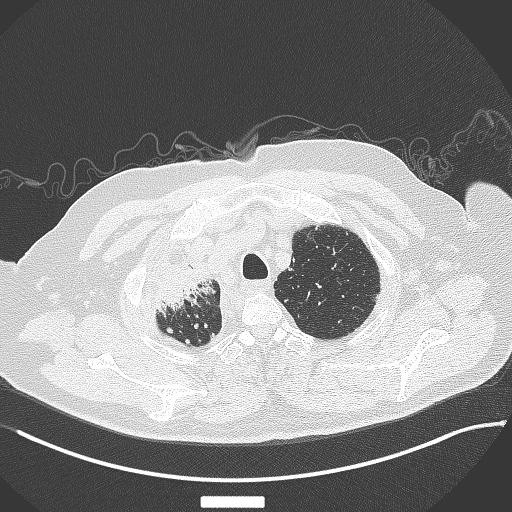
Chest CT, one axial slice; position 319 of 384 along the scan axis; reconstruction kernel B70f; lung window (W 1500 / L -600 HU); 512 × 512 image matrix, field of view 400 × 400 mm. Patient: male, 69 years. Case-level facts recorded for this patient, not image findings: clinical TNM (as recorded): T4 N3 M1.
Outlined on this slice (bounding box drawn by a radiologist):
- lung tumour (recorded histology: adenocarcinoma): bounding box [x1, y1, x2, y2] px = [152, 257, 216, 318]